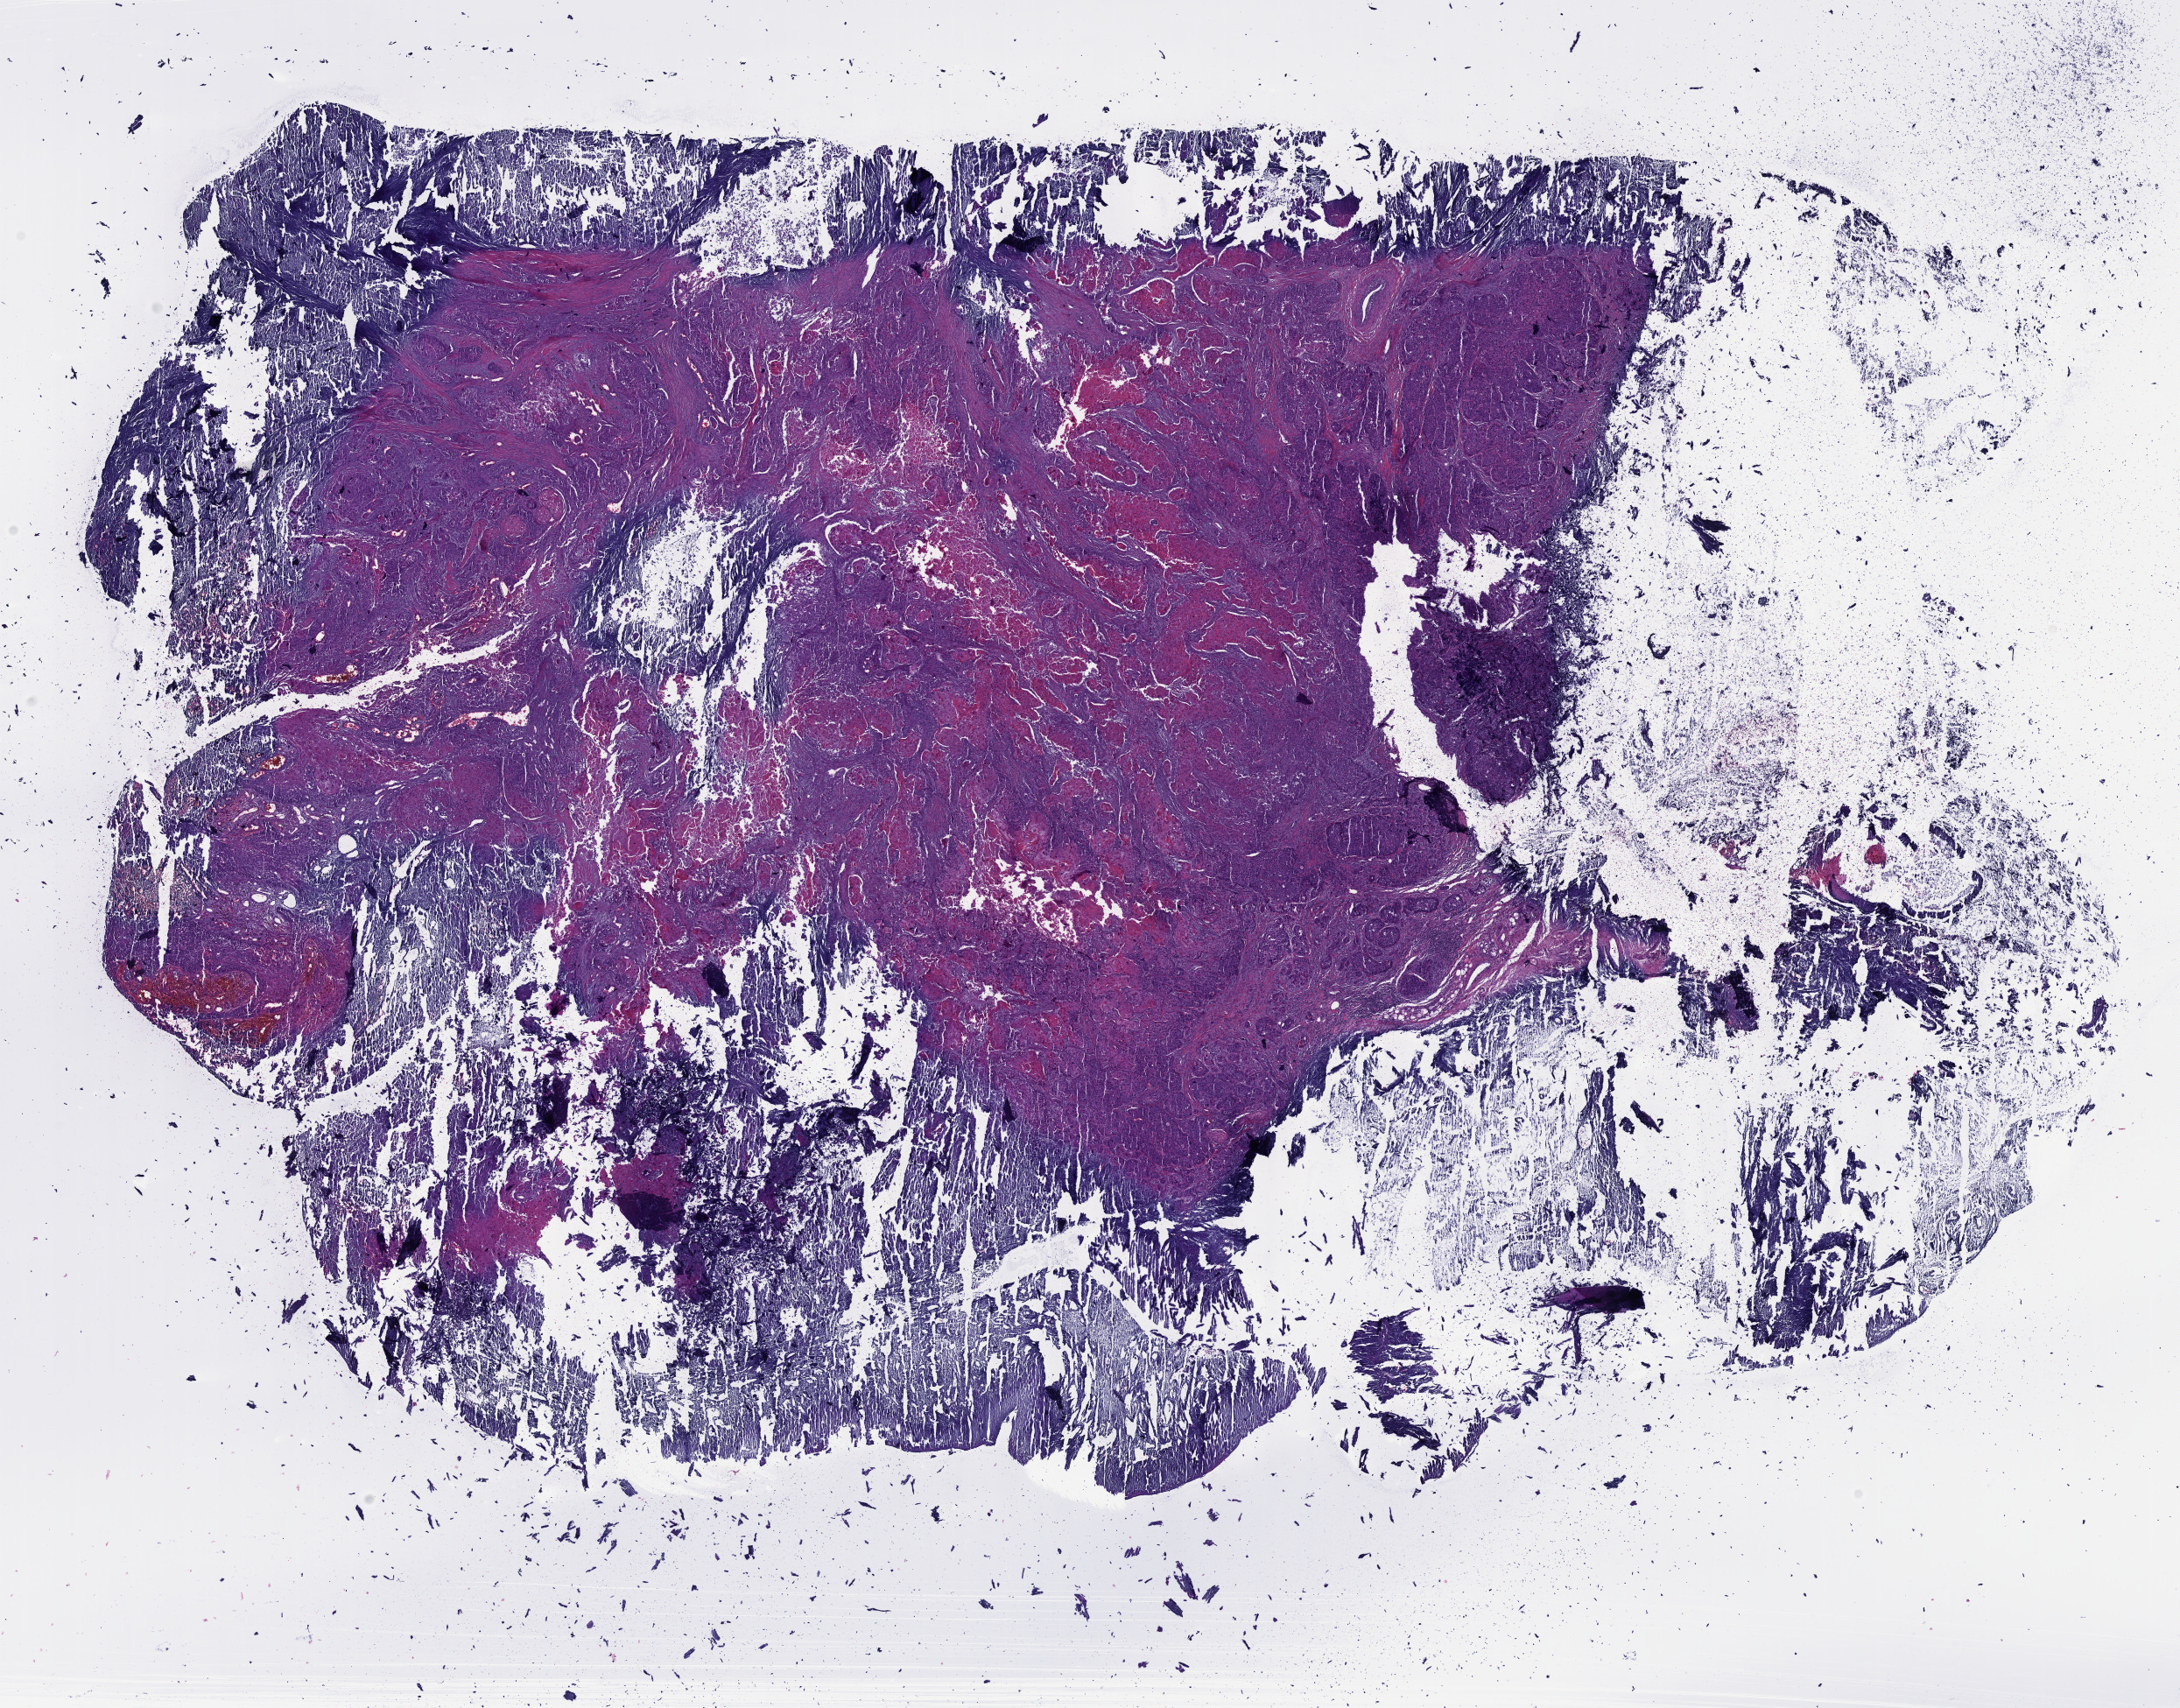
Hematoxylin and eosin (H&E) stained whole-slide image — shown as a low-resolution overview of the whole scanned area (about 20.1 x 15.8 mm), formalin-fixed paraffin-embedded (FFPE) diagnostic section, sample: primary tumour, head and neck. Male patient; age at initial diagnosis 67 years.
Histologic diagnosis: Squamous cell carcinoma, NOS (larynx, NOS).